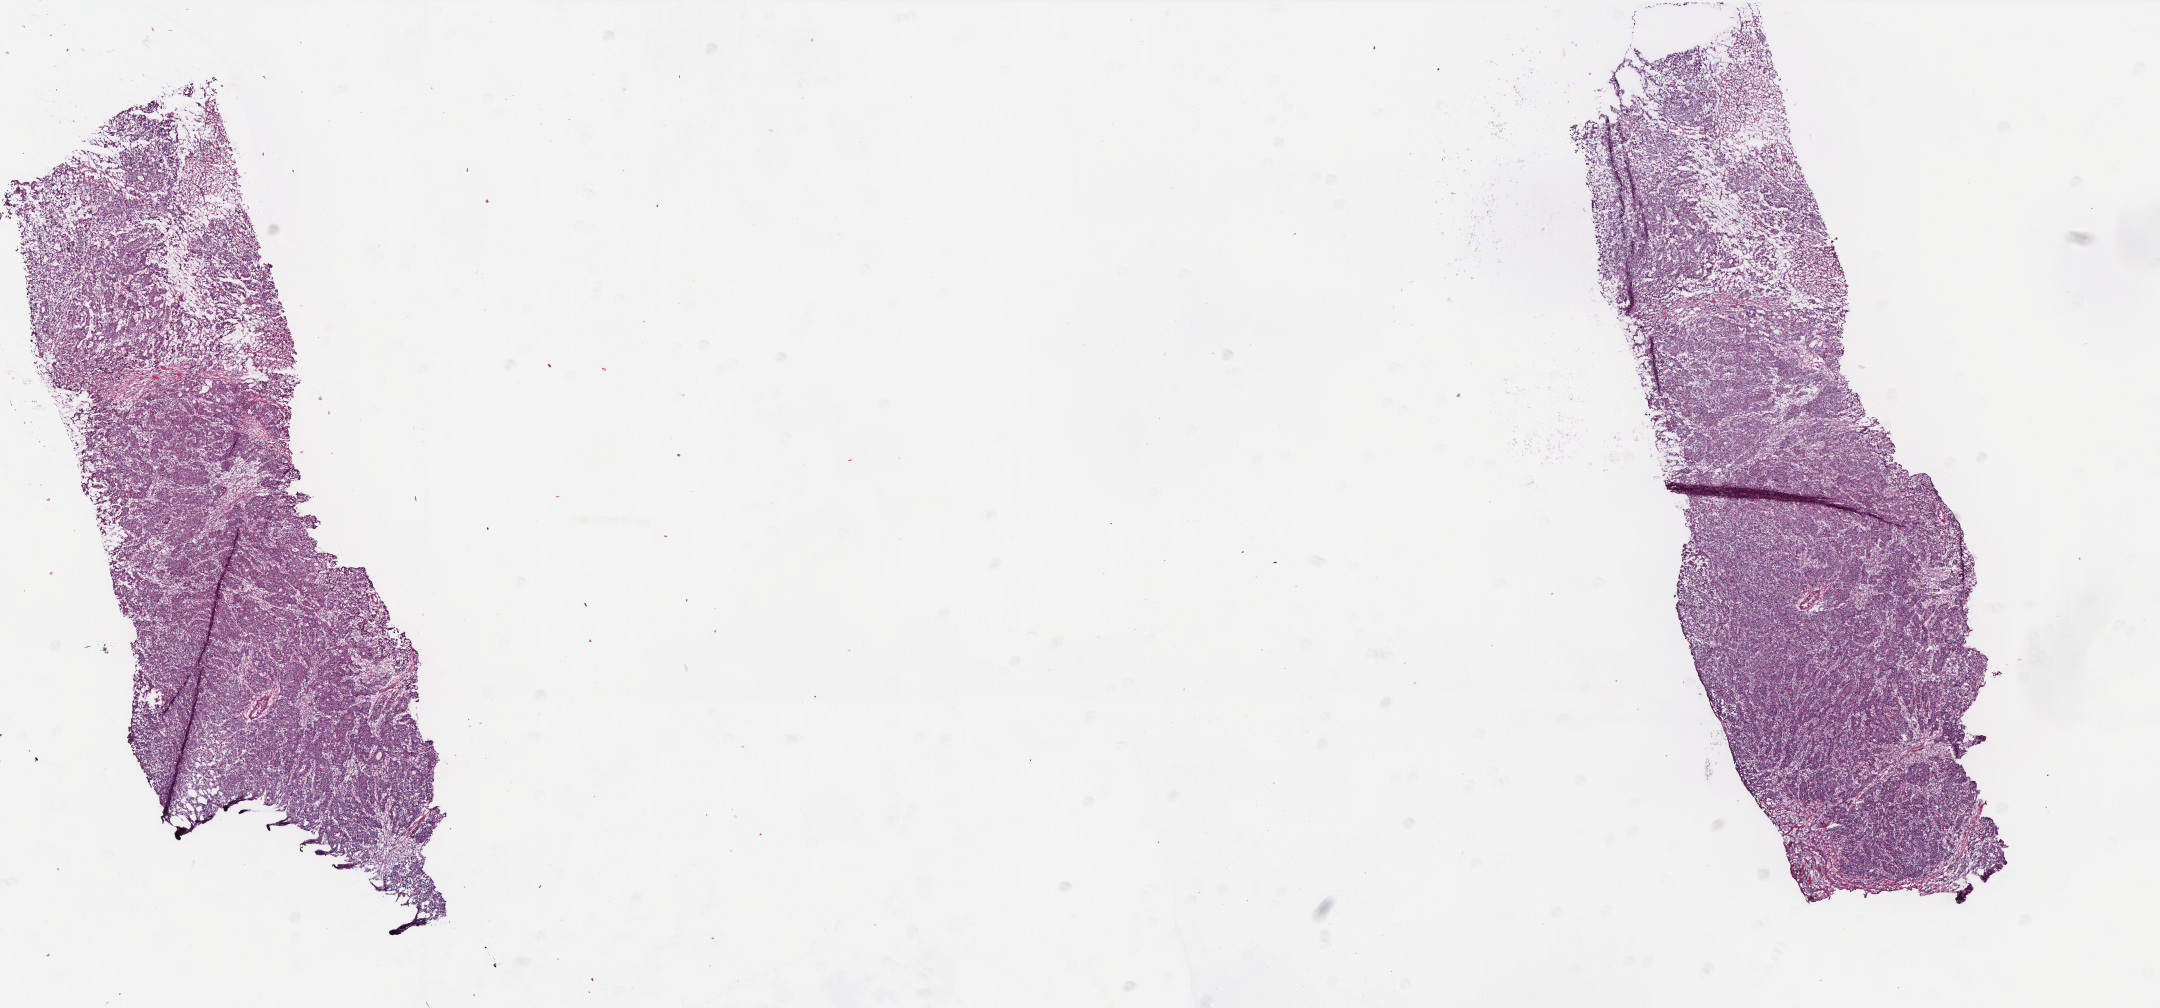
Hematoxylin and eosin (H&E) stained whole-slide image, shown as a low-resolution overview of the whole scanned area (about 17.3 x 8.1 mm). Frozen section. Colon, primary tumour sample. Female patient; age at initial diagnosis 88 years.
Pathologic diagnosis: Adenocarcinoma, NOS (cecum).